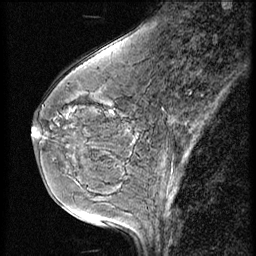
Breast MRI (dynamic contrast-enhanced), one sagittal slice; slice 18 of 56 in the series (ordered by position); 3 images stored at this slice position (order not interpretable as contrast timing); 1.5 T; TE 4.2 ms, TR 9 ms; 256 × 256 image matrix. Patient: female, 49 years. From the clinical record (not read from this slice): setting: breast cancer imaged before/during neoadjuvant chemotherapy; receptor status: HER2-positive.
Outlined on this slice (semi-automatically segmented with operator editing):
- analysis volume of interest (the breast-tissue region the enhancement analysis was run in; not a lesion): bounding box [x1, y1, x2, y2] px = [32, 75, 128, 193]
- tumour enhancement mask (voxels above the 140 % enhancement threshold inside the analysis volume of interest): [32, 132, 35, 137]